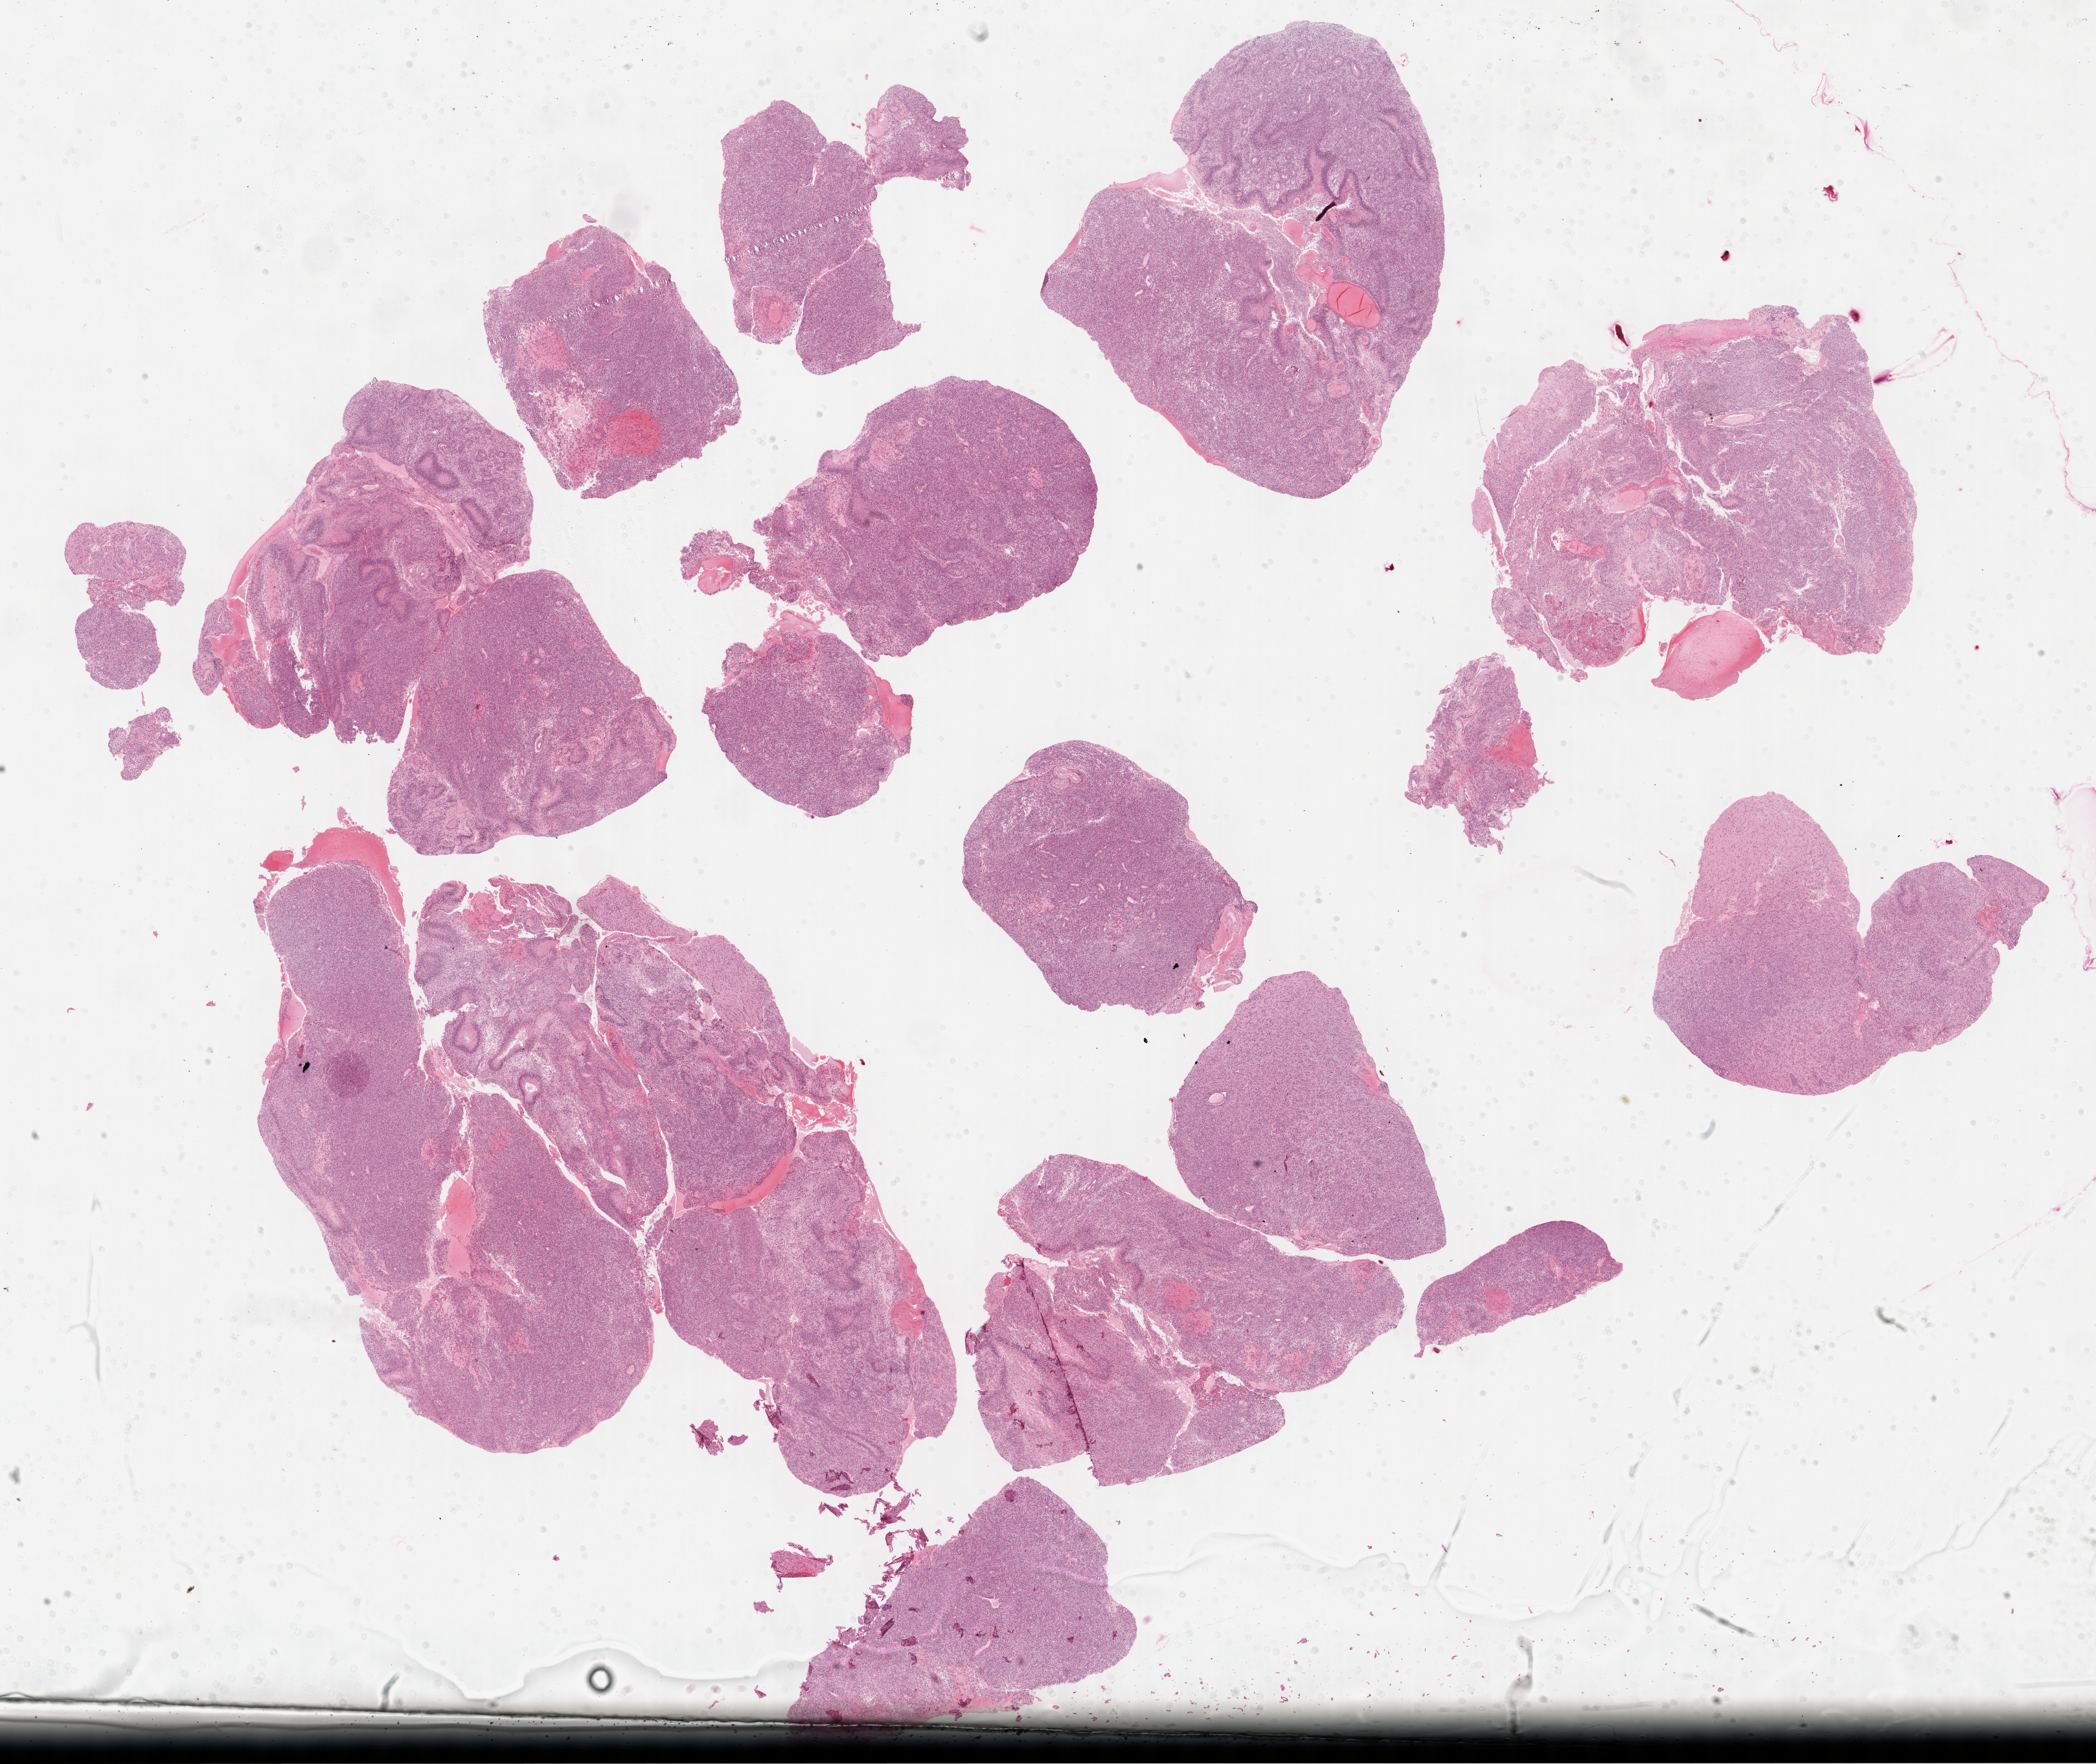
Whole-slide histology image, H&E-stained, shown as a low-resolution overview of the whole scanned area (about 26.2 x 22.0 mm). Formalin-fixed paraffin-embedded (FFPE) diagnostic section. Brain, primary tumour sample. Male patient; age at initial diagnosis 63 years.
* histologic diagnosis: Glioblastoma